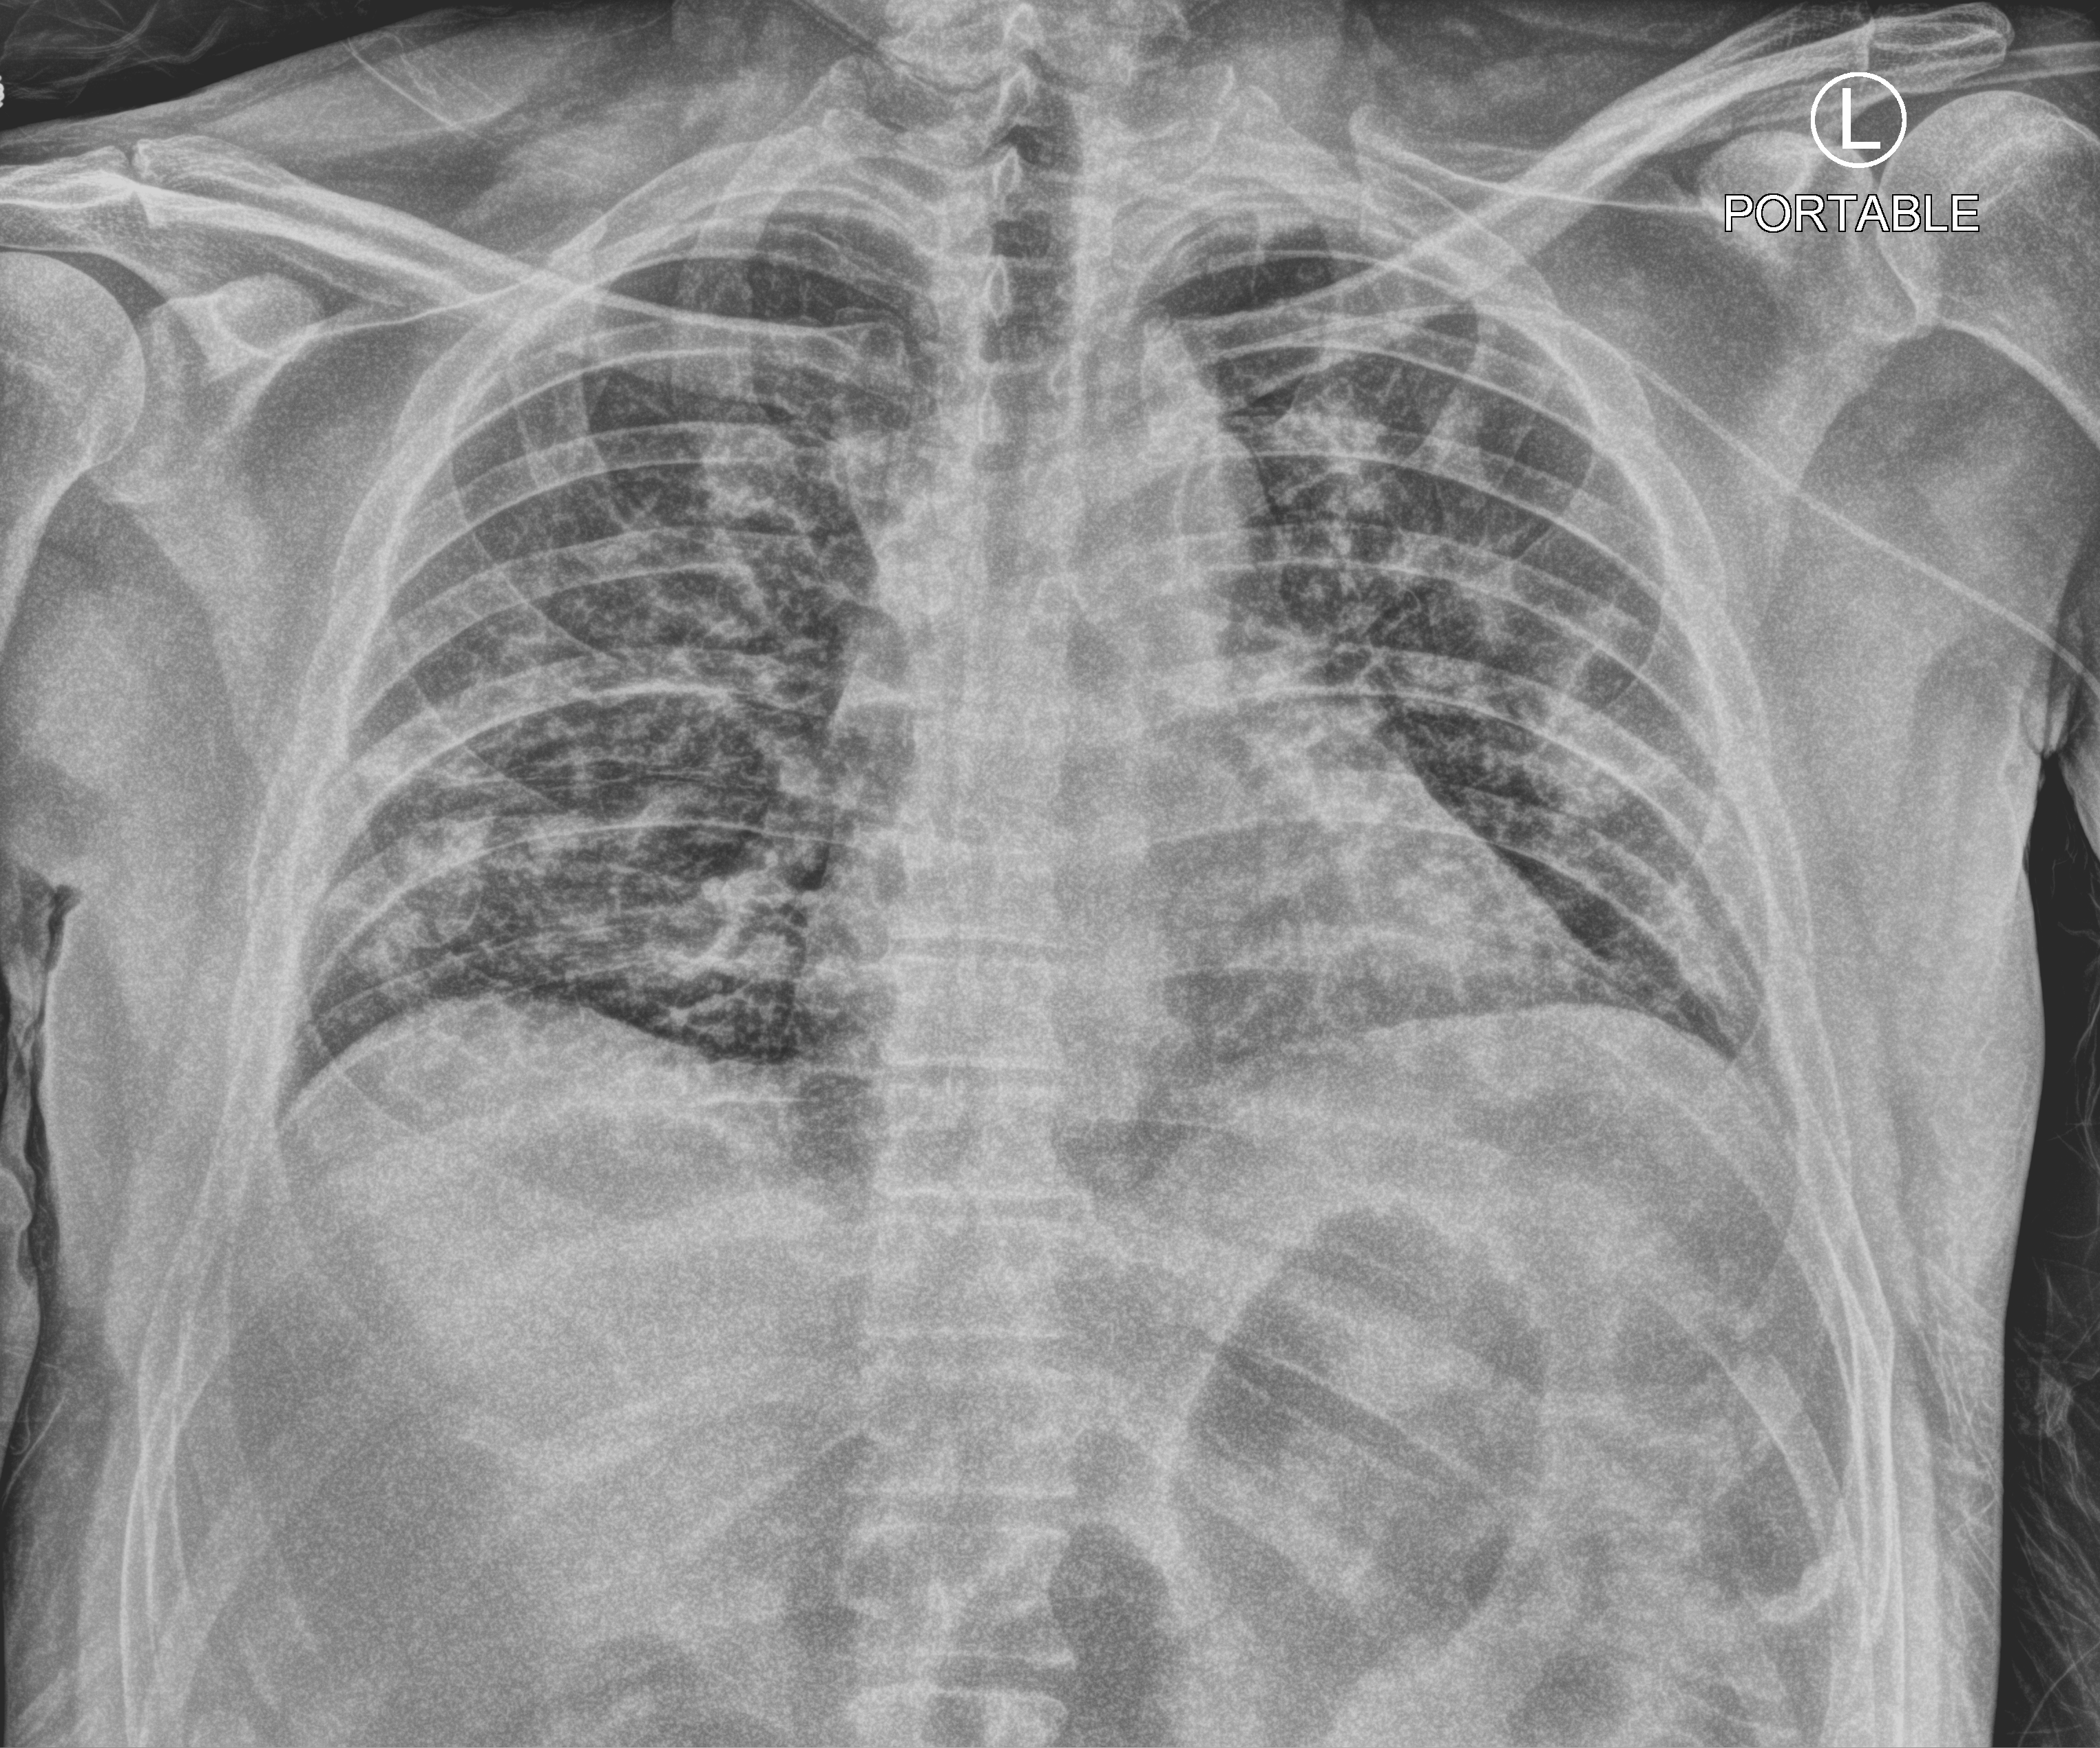
Portable chest radiograph; anteroposterior (AP) projection. Patient hospitalised with COVID-19; male, aged 18–59 years.
From the hospital-stay record, not from the radiograph (when in the stay this image was taken is not recorded):
- hypertension (admission record): no
- mechanically ventilated during this hospital stay: no
- diabetes (admission record): no